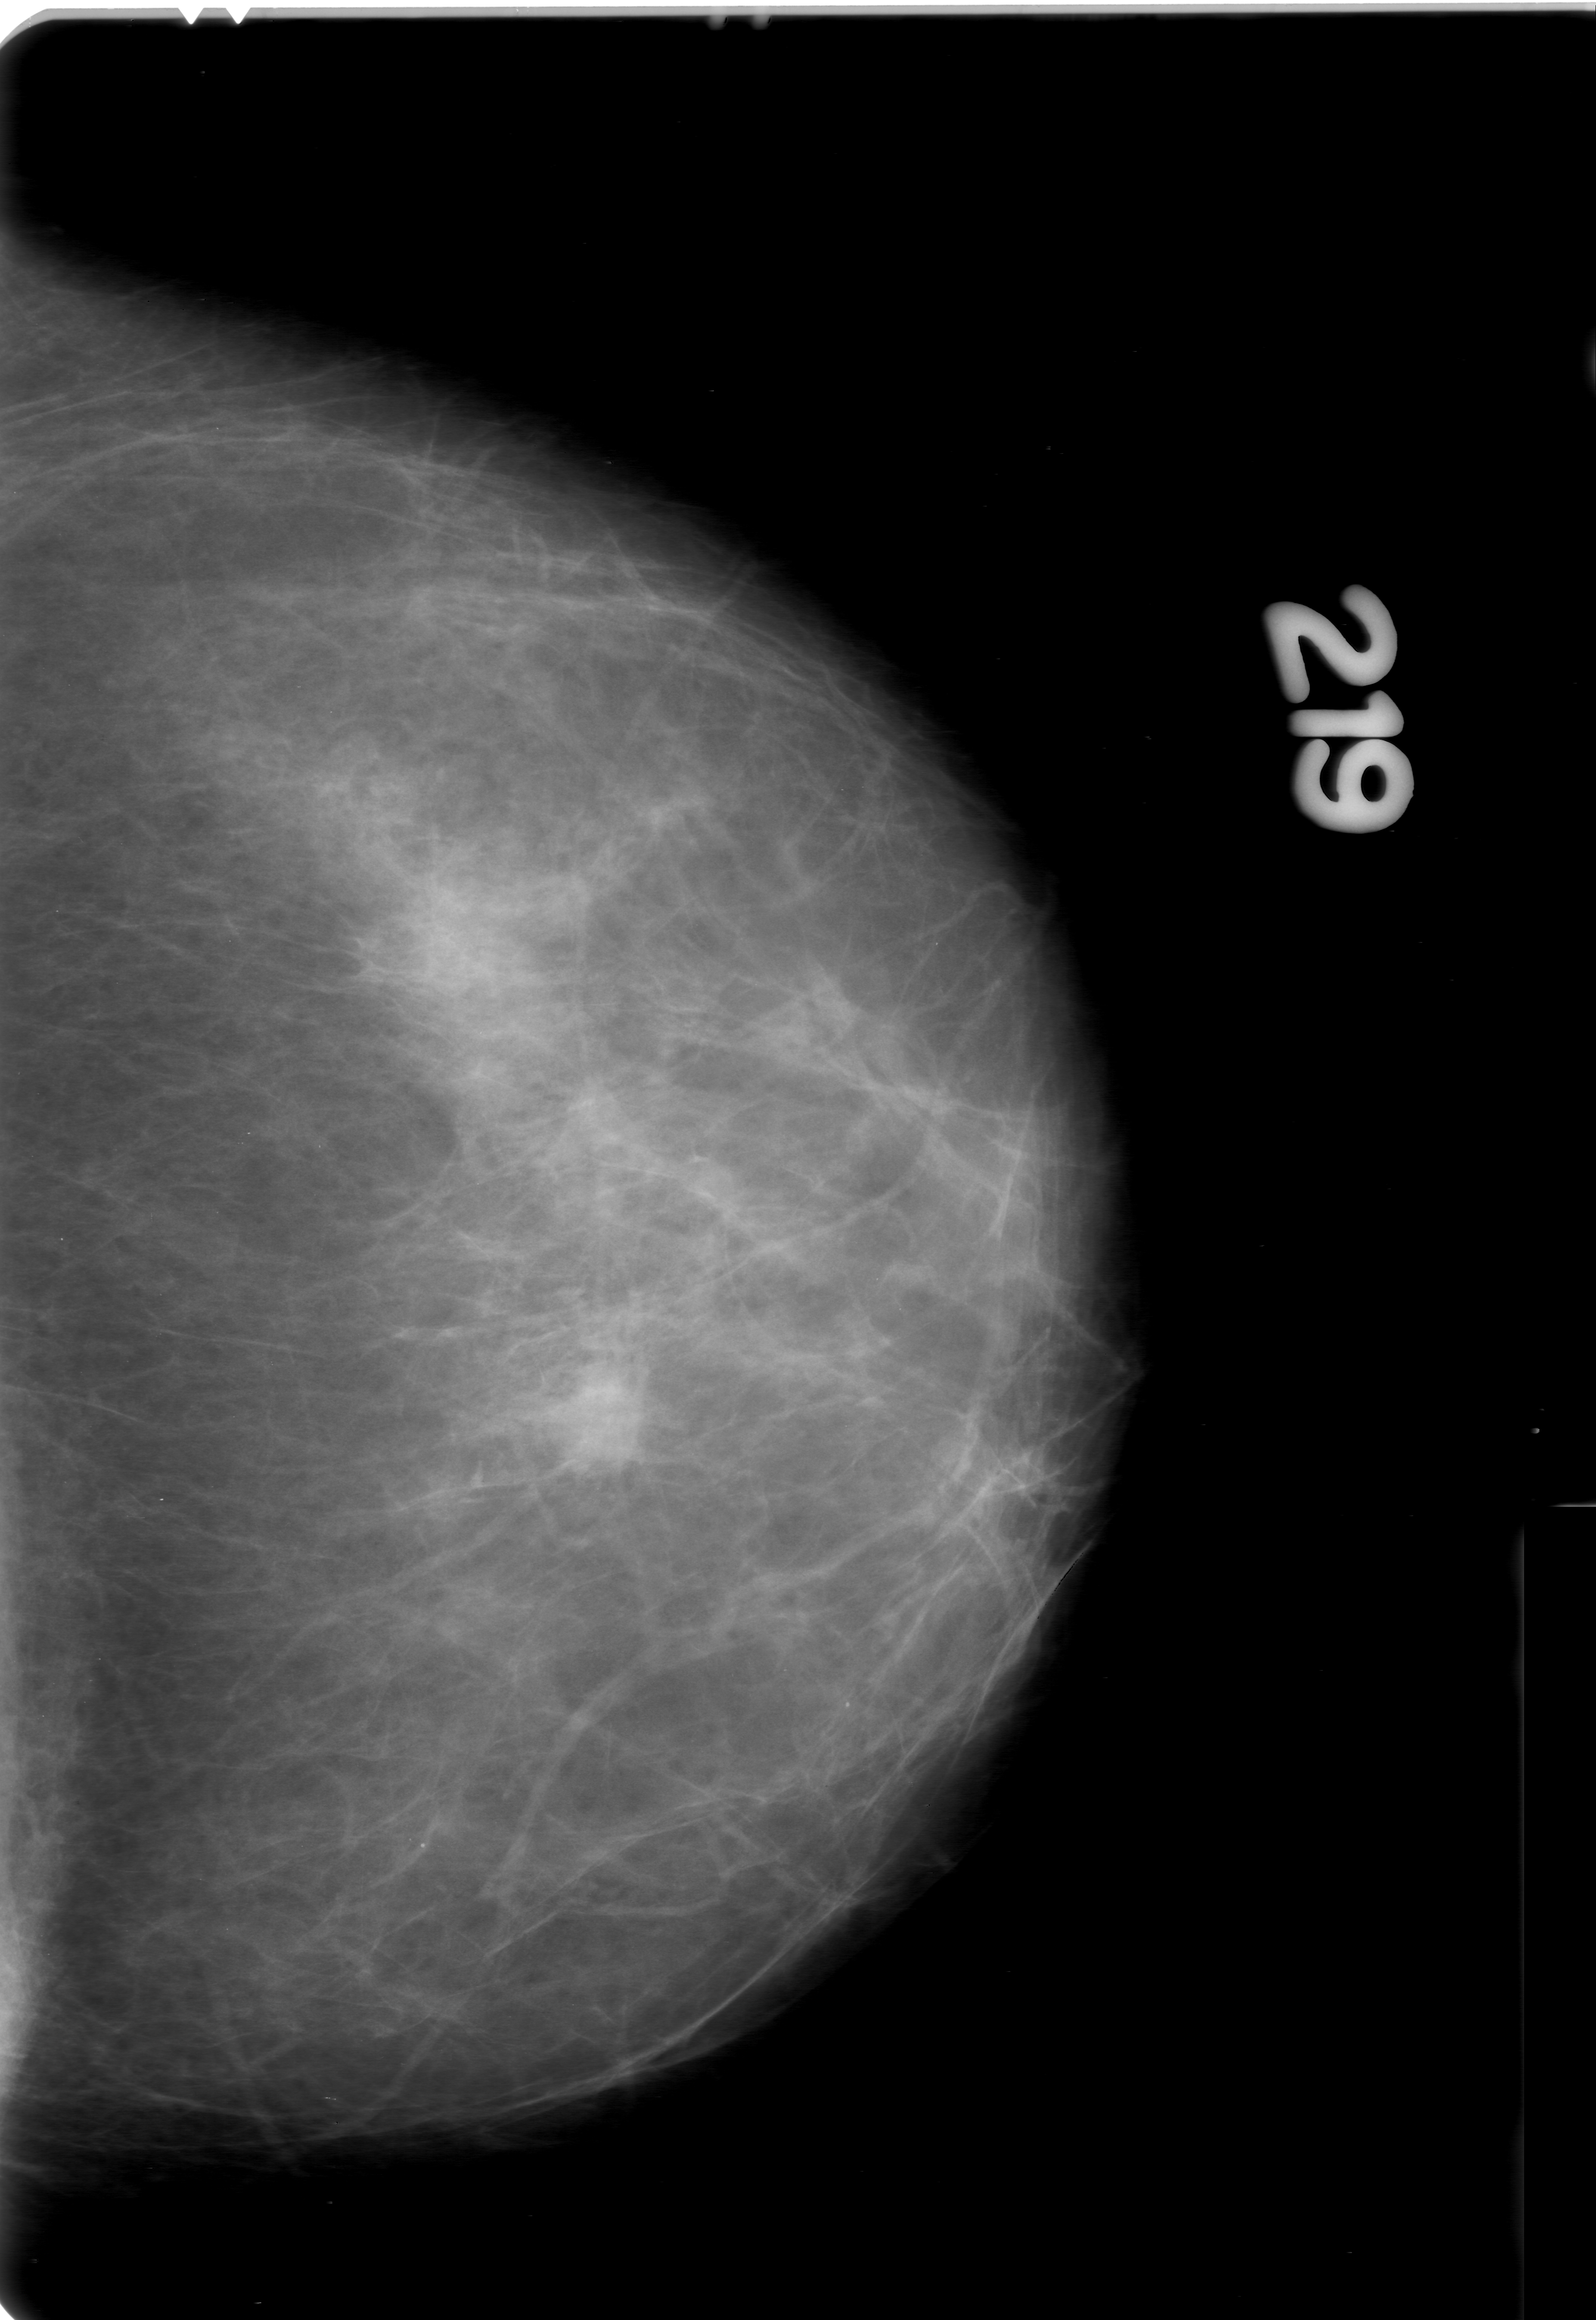
Mammogram (digitized film), left breast, craniocaudal (CC) view, breast composition: scattered fibroglandular densities (BI-RADS density category 2 of 4).
Abnormality record for this image: mass, shape oval, margins obscured; BI-RADS assessment category 4; pathology result (as recorded, not read from the image): malignant.